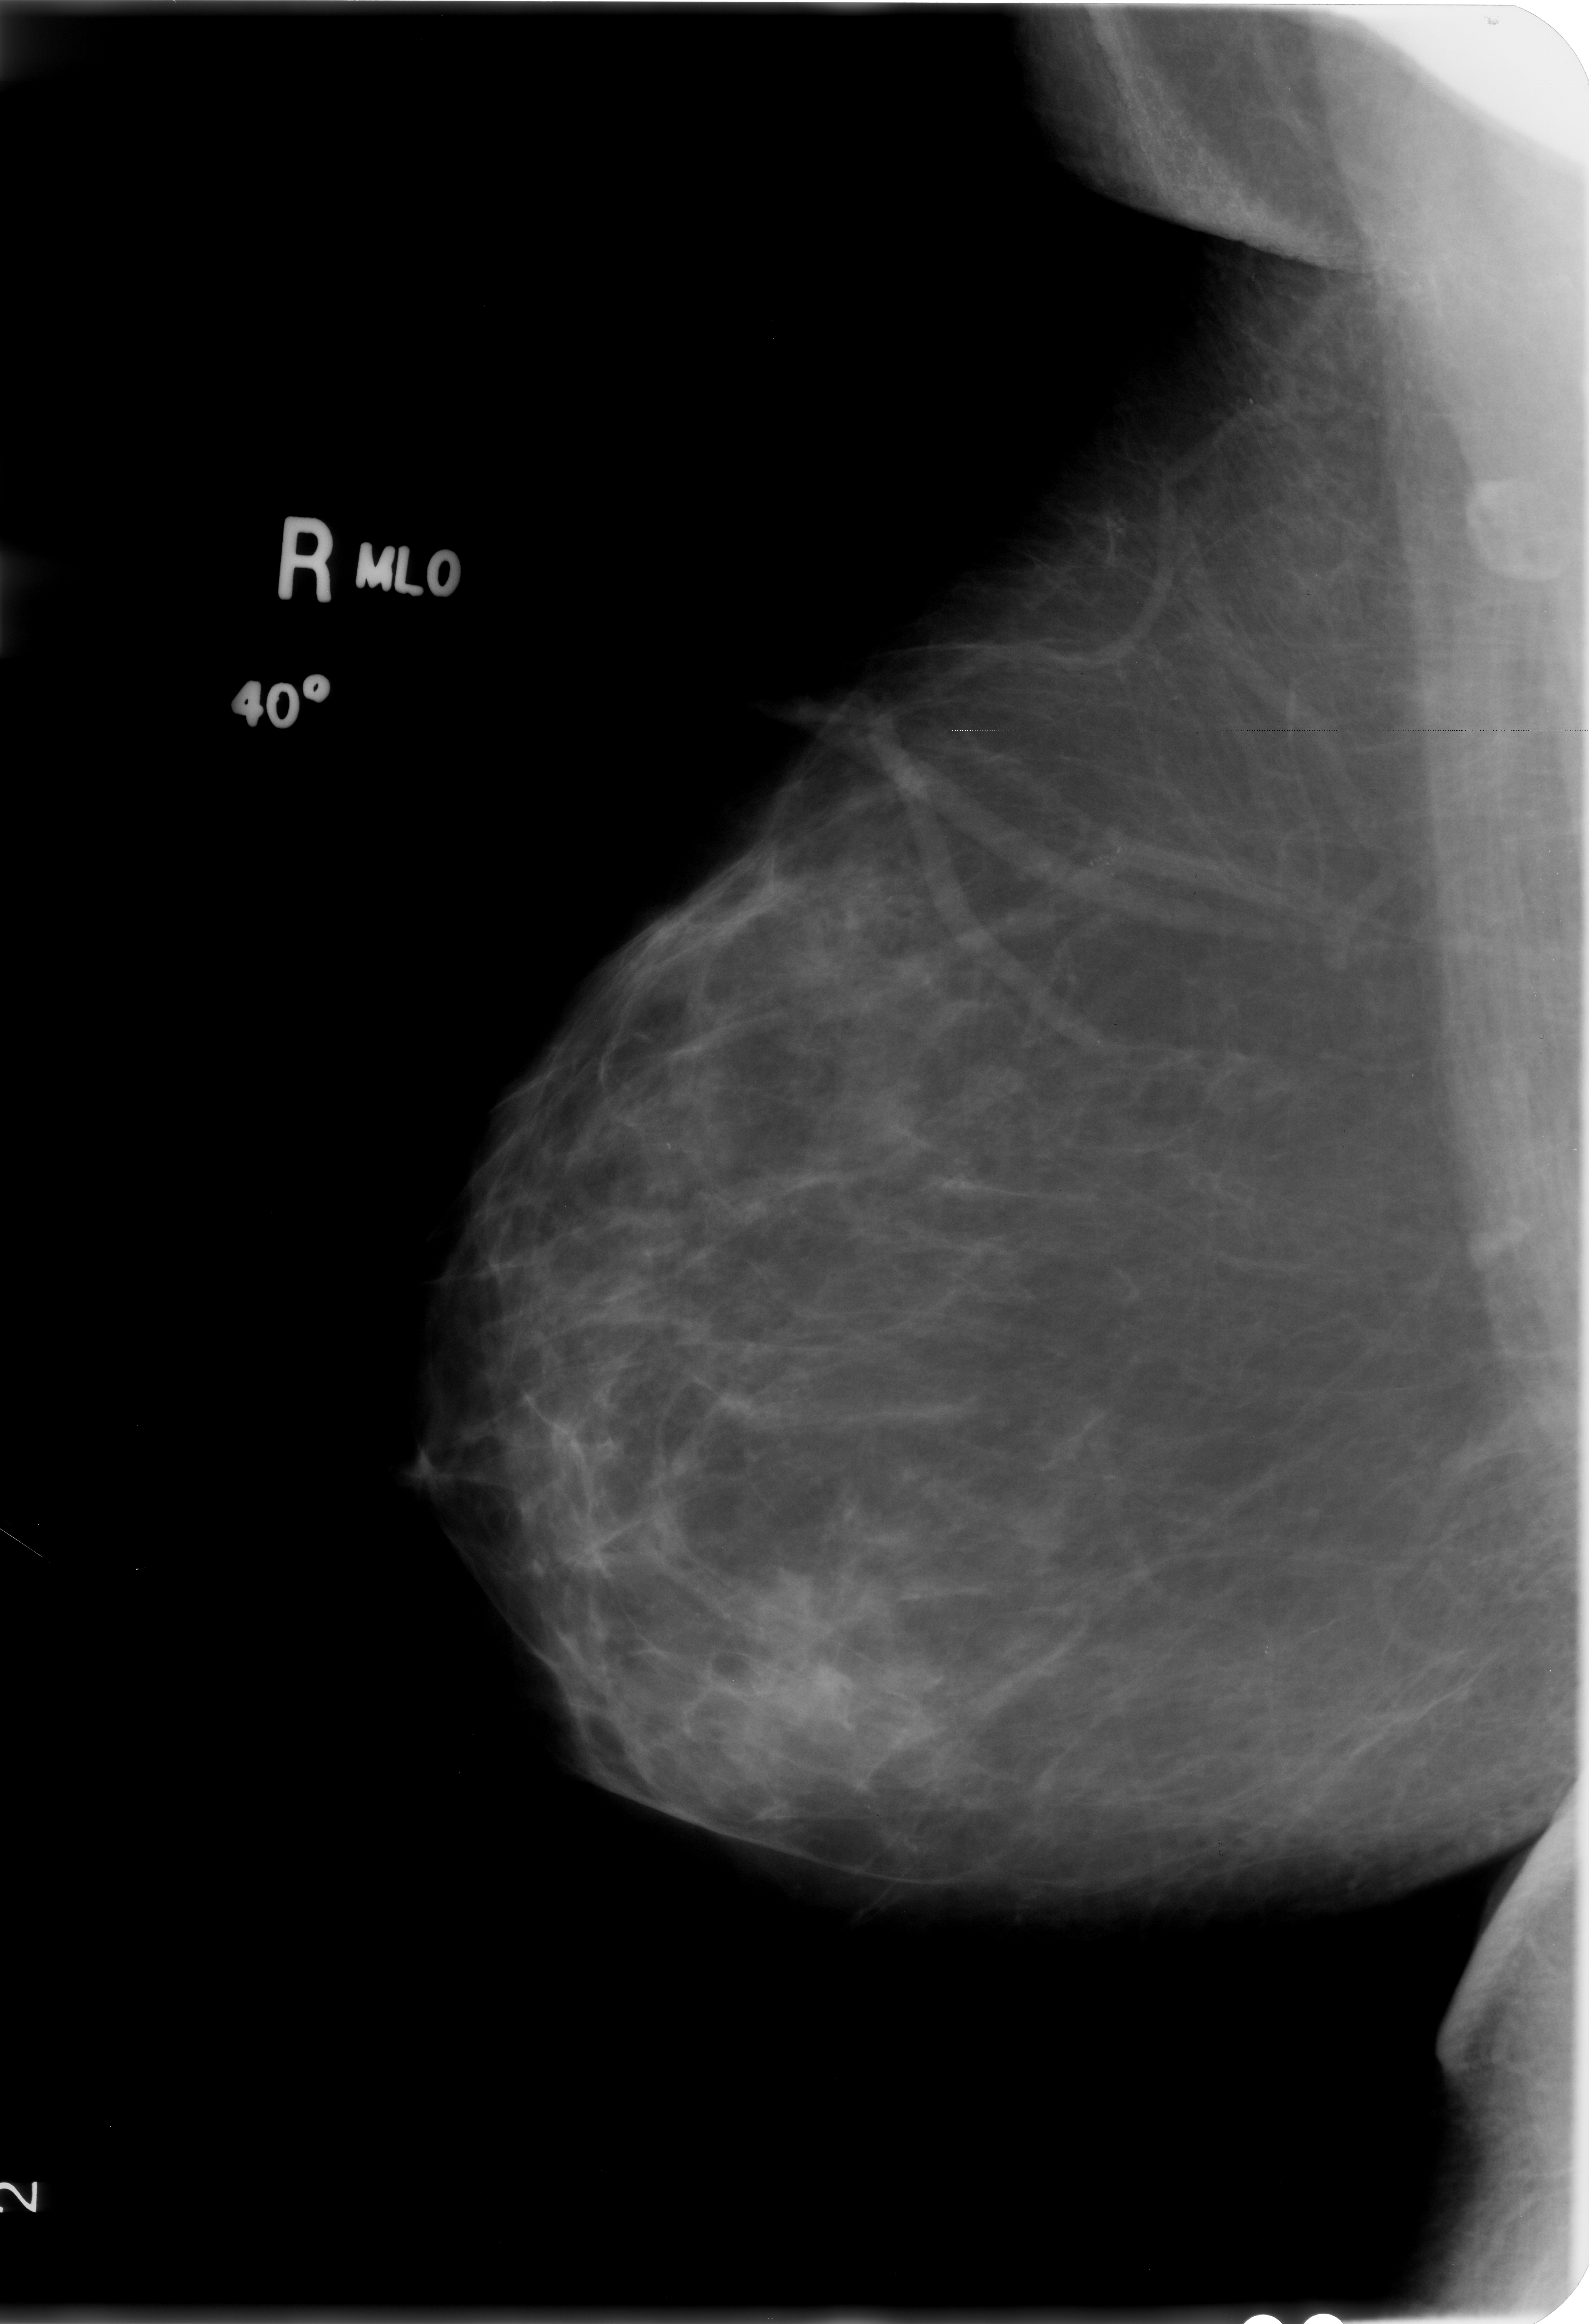
Scanned film-screen mammogram, right breast, mediolateral oblique (MLO) view.
Radiologist-marked abnormalities on this image: calcifications, morphology pleomorphic, distribution clustered; BI-RADS assessment category 4; subtlety rating 3 on a 1 (subtle) to 5 (obvious) scale; pathology (as recorded): benign.